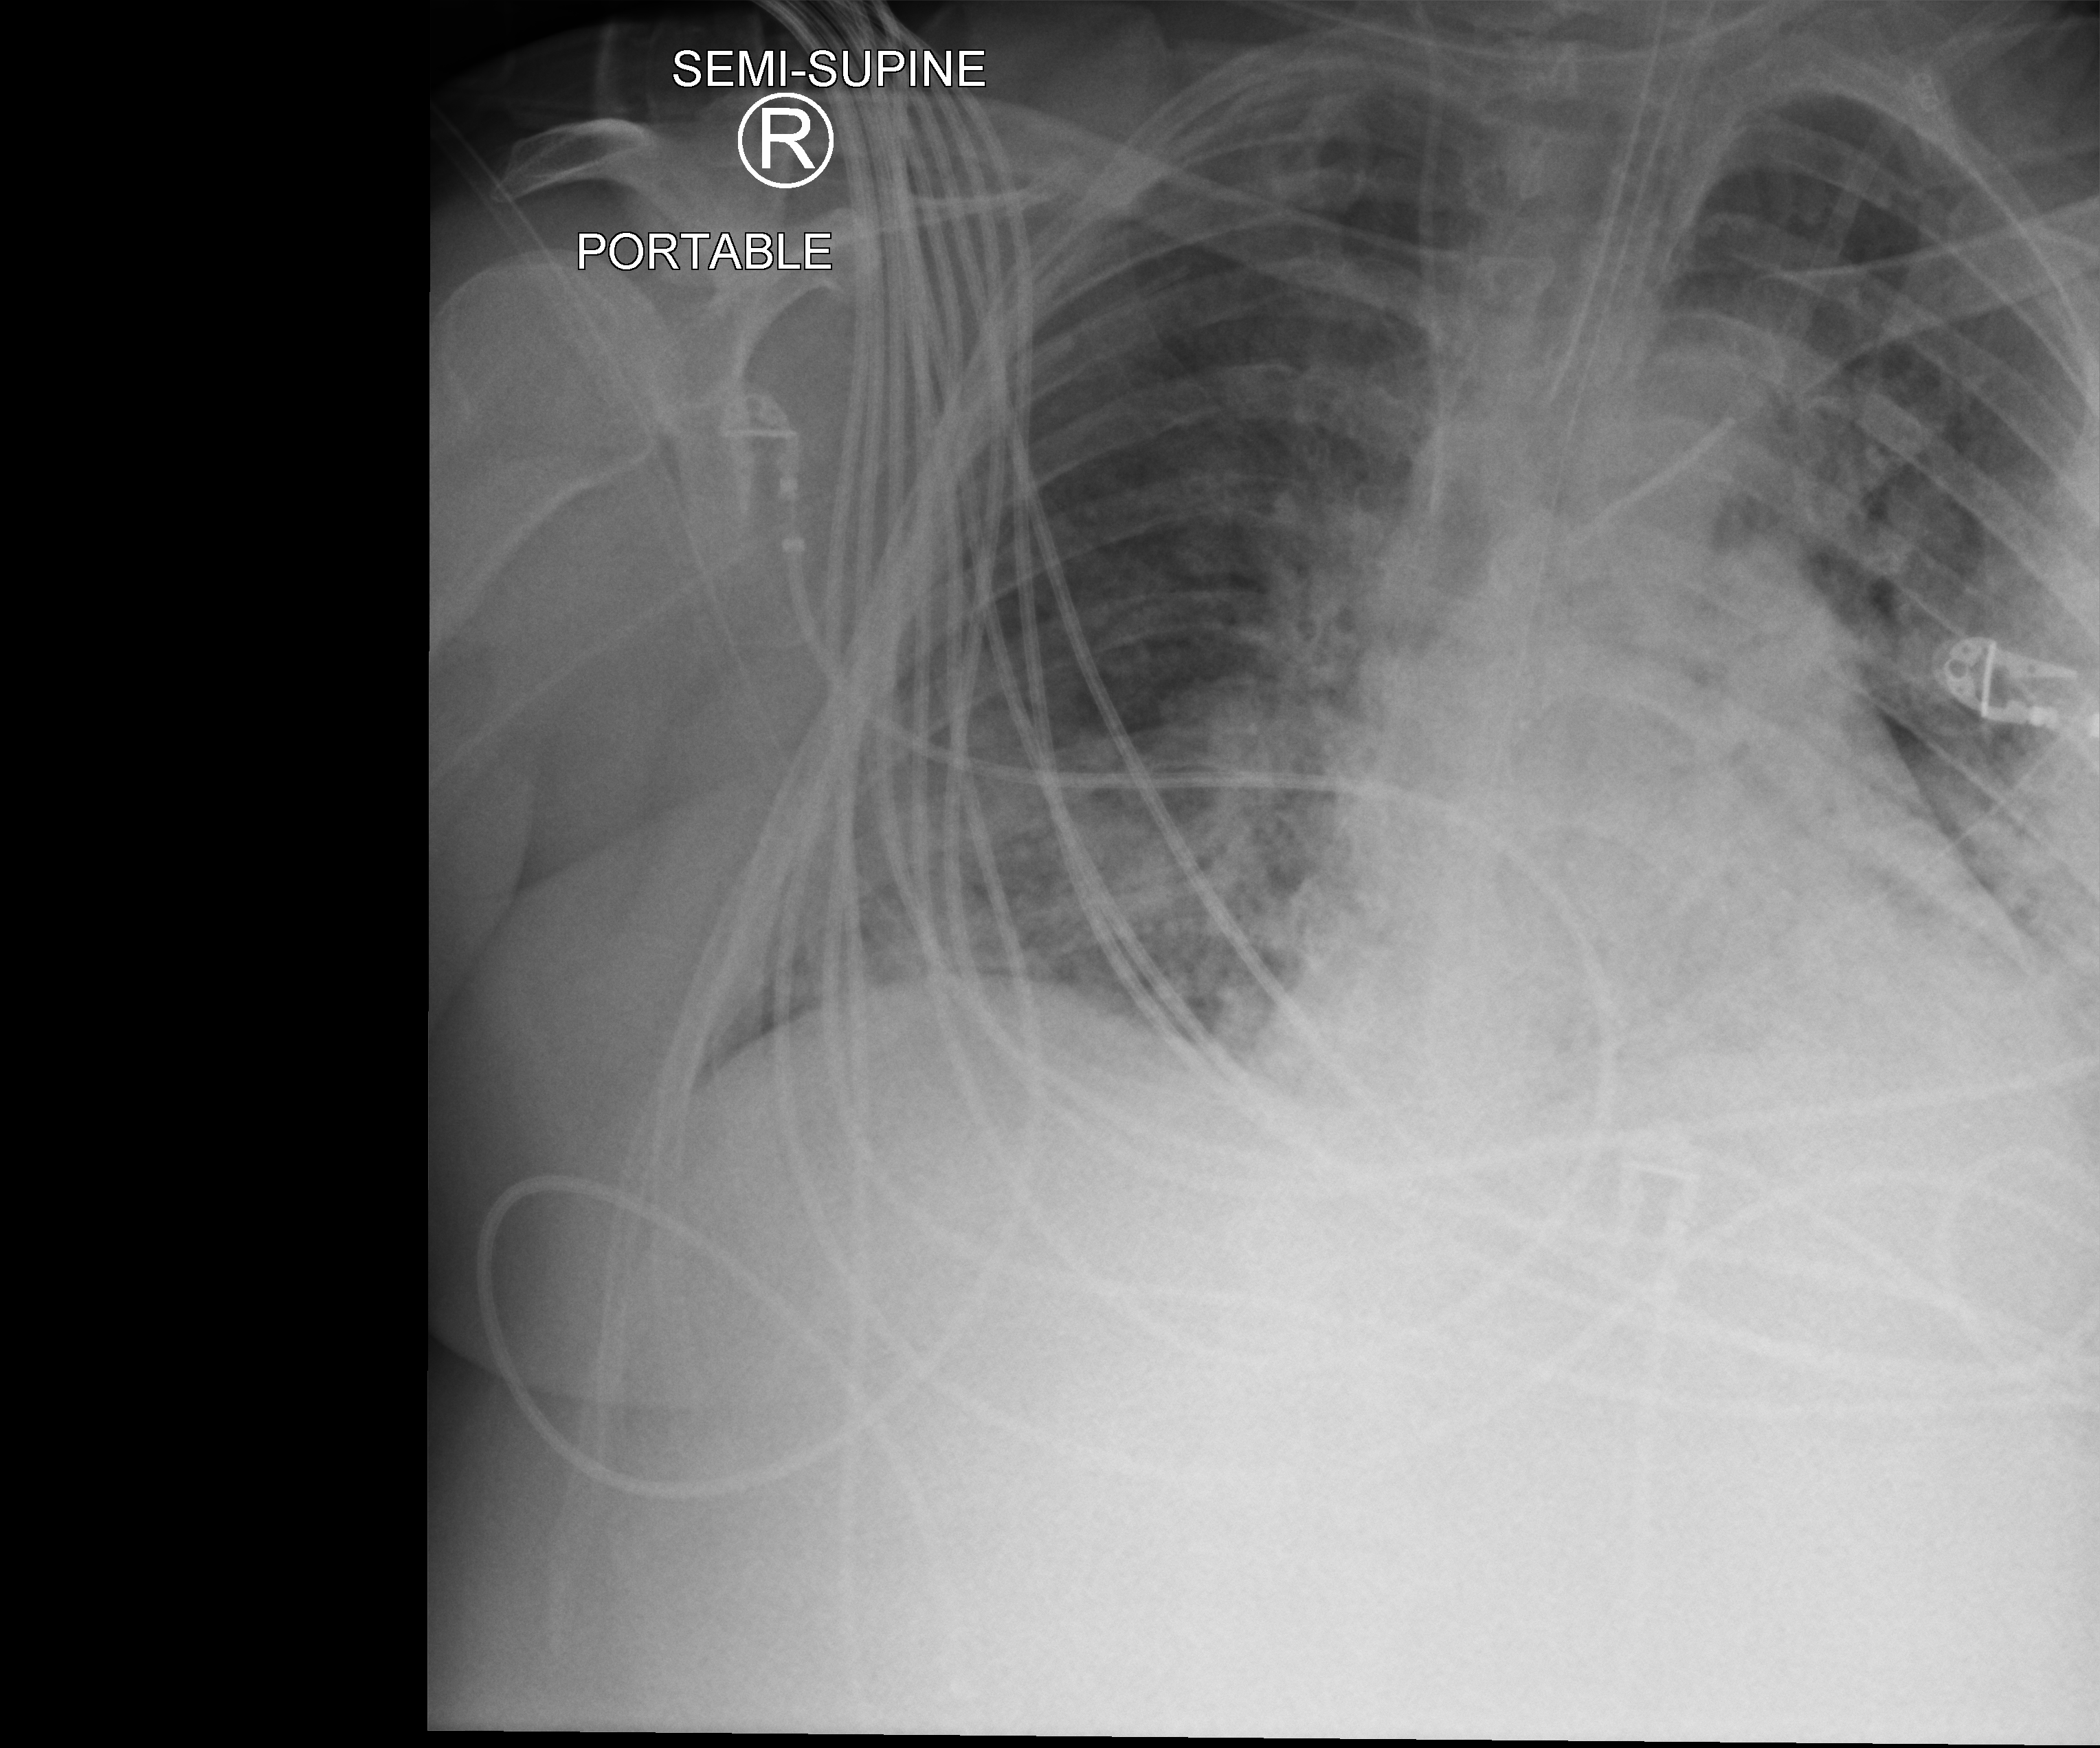
Portable chest radiograph; anteroposterior (AP) projection. Patient hospitalised with COVID-19; male, aged 18–59 years.
From the hospital-stay record, not from the radiograph (when in the stay this image was taken is not recorded): diabetes (admission record): no.